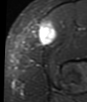
MRI of an extremity soft-tissue mass, one axial slice; slice 13 of 48 in the series (ordered by position); STIR; MR volume resampled by the dataset authors to the PET/CT grid (not the native acquisition matrix); 3.27 mm slice thickness; 87 × 102 image matrix, field of view 85 × 100 mm. Female patient. From the clinical record (not read from this slice): histological type: synovial sarcoma; grade: intermediate; site of the primary tumour: right thigh.
Structures marked on this image (expert contour drawn on MRI and transferred to this co-registered scan by the dataset authors):
- gross tumour volume including surrounding oedema: bounding box [x1, y1, x2, y2] px = [38, 22, 57, 44]
- gross tumour volume (mass): [38, 22, 57, 46]